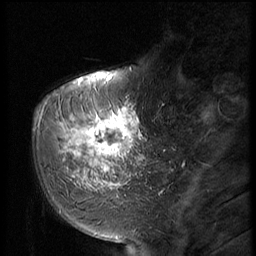
Breast MRI (dynamic contrast-enhanced), one sagittal slice; position 17 of 56 along the scan axis; dynamic contrast-enhanced series, image 2 of 2 at this slice position (ordered by acquisition); 1.5 T; TE 4.2 ms, TR 9 ms; 2.5 mm slice thickness; 256 × 256 image matrix, field of view 180 × 180 mm. Female patient, age 51 years. Case-level facts recorded for this patient, not image findings: setting: breast cancer imaged before/during neoadjuvant chemotherapy; receptor status: triple-negative.
Annotated regions visible in this slice (semi-automatically segmented with operator editing):
- analysis volume of interest (the breast-tissue region the enhancement analysis was run in; not a lesion): bounding box <60,98,147,197> (left, top, right, bottom; pixels)
- tumour enhancement mask (voxels above the 140 % enhancement threshold inside the analysis volume of interest): <70,108,141,189>